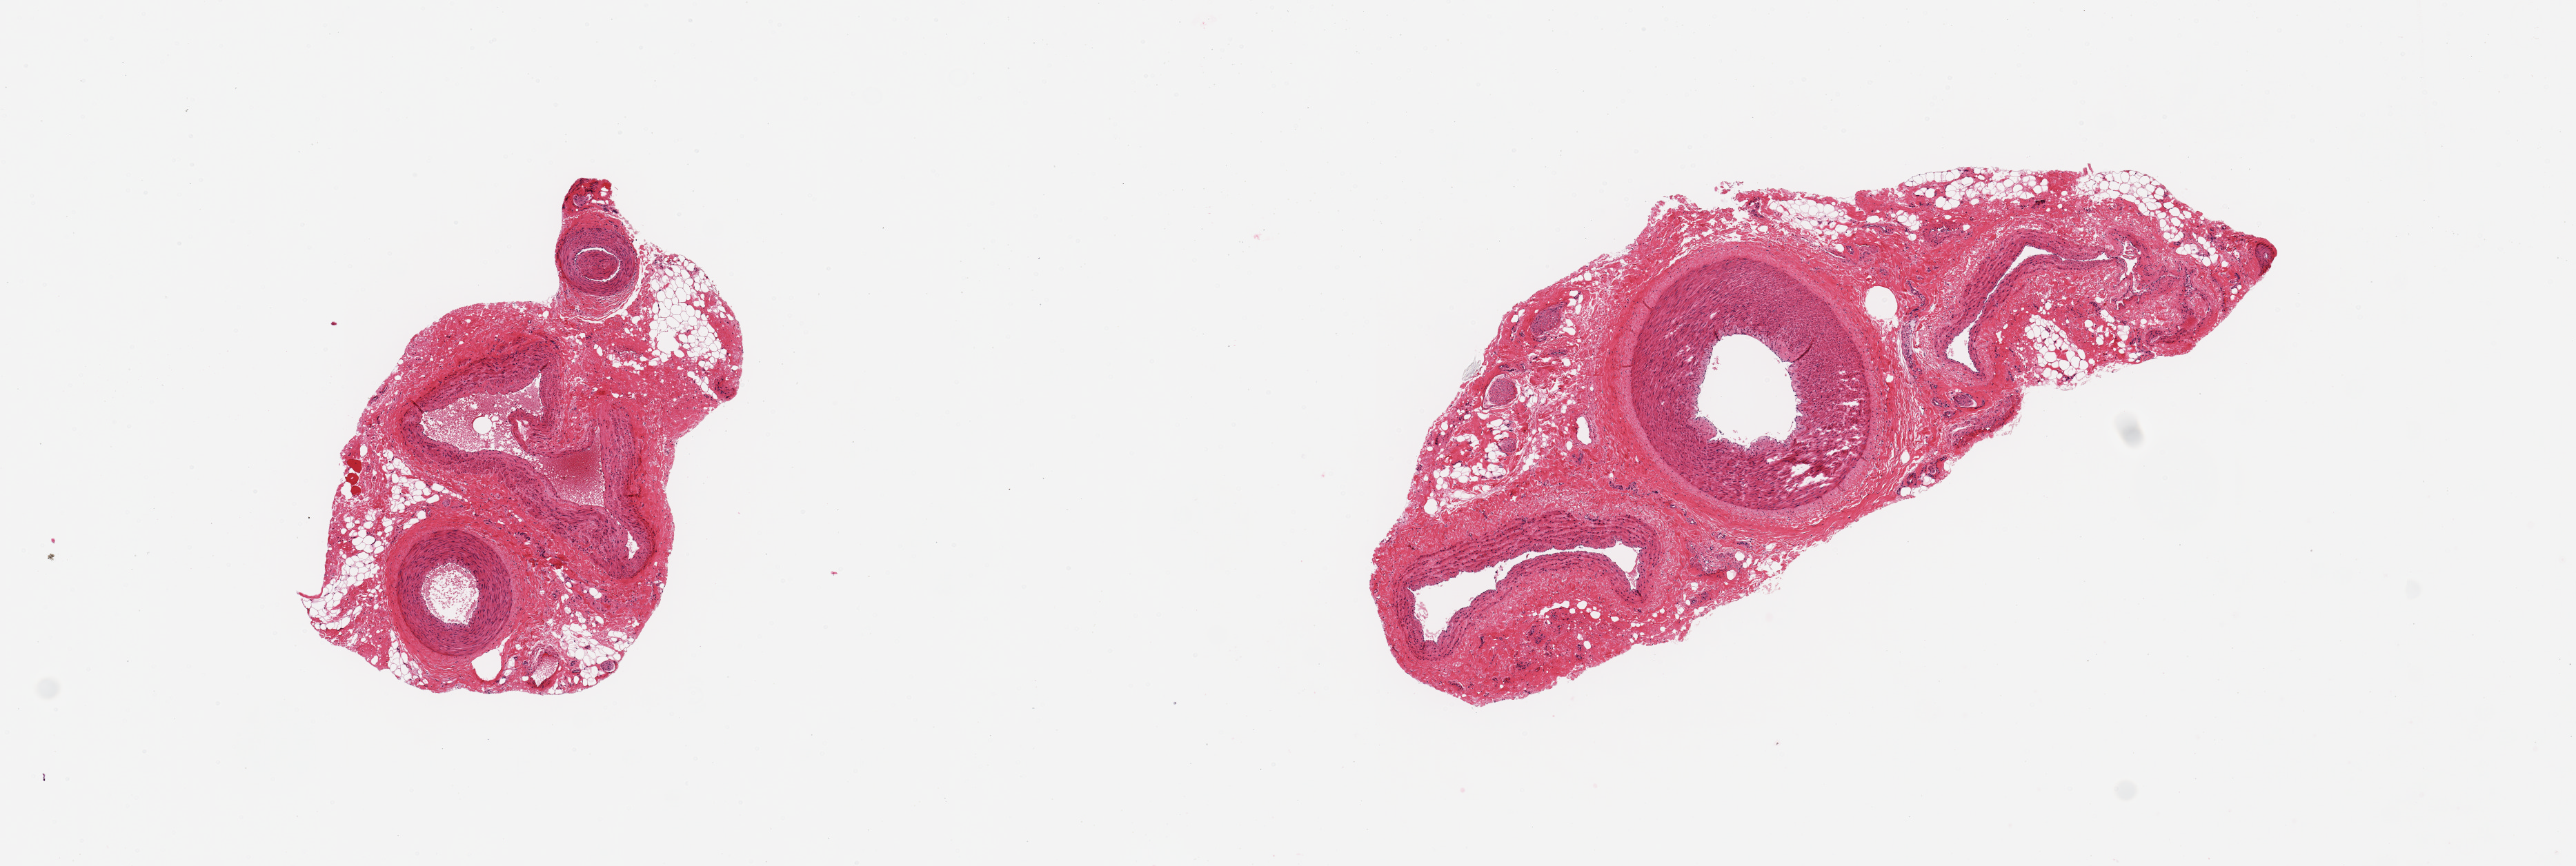
Haematoxylin and eosin whole-slide image, low-resolution overview of the scanned area, about 14.8 x 5.0 mm (slide scanned at 20x); PAXgene-fixed, paraffin-embedded tissue; sampled site (target tissue): tibial artery; tissue donor sample. Donor sex: female.
Pathologist's review note for this sample: 2 pieces, 5.5x2 mm 2 veins and 1 artery& 3x2 mm 2 arteries & 1 vein; up to 30% adipose.